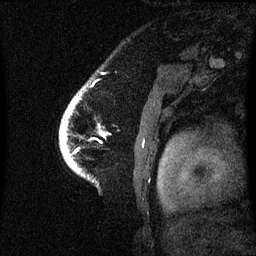
Breast MRI (dynamic contrast-enhanced), one sagittal slice; position 53 of 60 along the scan axis; dynamic contrast-enhanced series, image 2 of 3 at this slice position (ordered by acquisition); 1.5 T; TE 4.2 ms, TR 8.4 ms; 2.1 mm slice thickness; 256 × 256 image matrix. Female patient, age 53 years. From the clinical record (not read from this slice): setting: breast cancer imaged before/during neoadjuvant chemotherapy; receptor status: HR-positive, HER2-negative.
Outlined on this slice (semi-automatically segmented with operator editing):
- analysis volume of interest (the breast-tissue region the enhancement analysis was run in; not a lesion): box from (x=61, y=100) to (x=105, y=171) px
- tumour enhancement mask (voxels above the 70 % enhancement threshold inside the analysis volume of interest): (x=62, y=114)–(x=69, y=147)